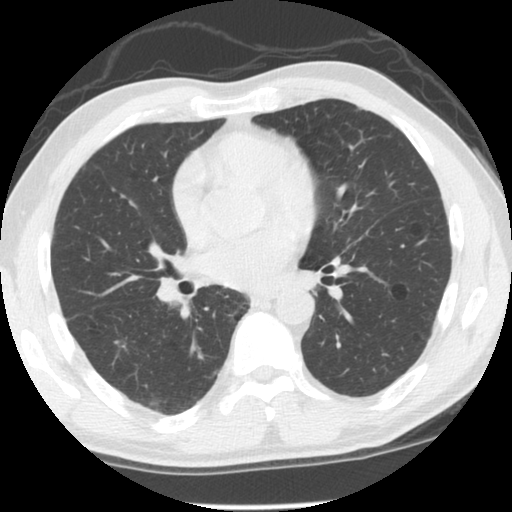
Low-dose screening chest CT, axial slice. Baseline screening round. Lung window (W 1500 / L -600 HU). Standard (soft-tissue) reconstruction kernel (STANDARD). Slice 57 of 125 in the series. Male, age 60 years at enrolment. Former smoker at enrolment.
Expert-annotated lung lesion, bounding box <93,324,146,370> (left, top, right, bottom; pixels). Reader record for this screening exam (exam-level; its link to the box is not recorded): non-calcified nodule or mass ≥4 mm, right lower lobe, 9 × 7 mm, spiculated (stellate) margins. Official screen result: positive, change unspecified: nodule(s) >= 4 mm or enlarging nodule(s), mass(es), or other non-specific abnormalities suspicious for lung cancer. Participant outcome: lung cancer diagnosed 534 days after this screen (after the second annual screen) — adenocarcinoma, NOS, right lower lobe, stage IA (AJCC 6th edition), 18 mm at pathology.